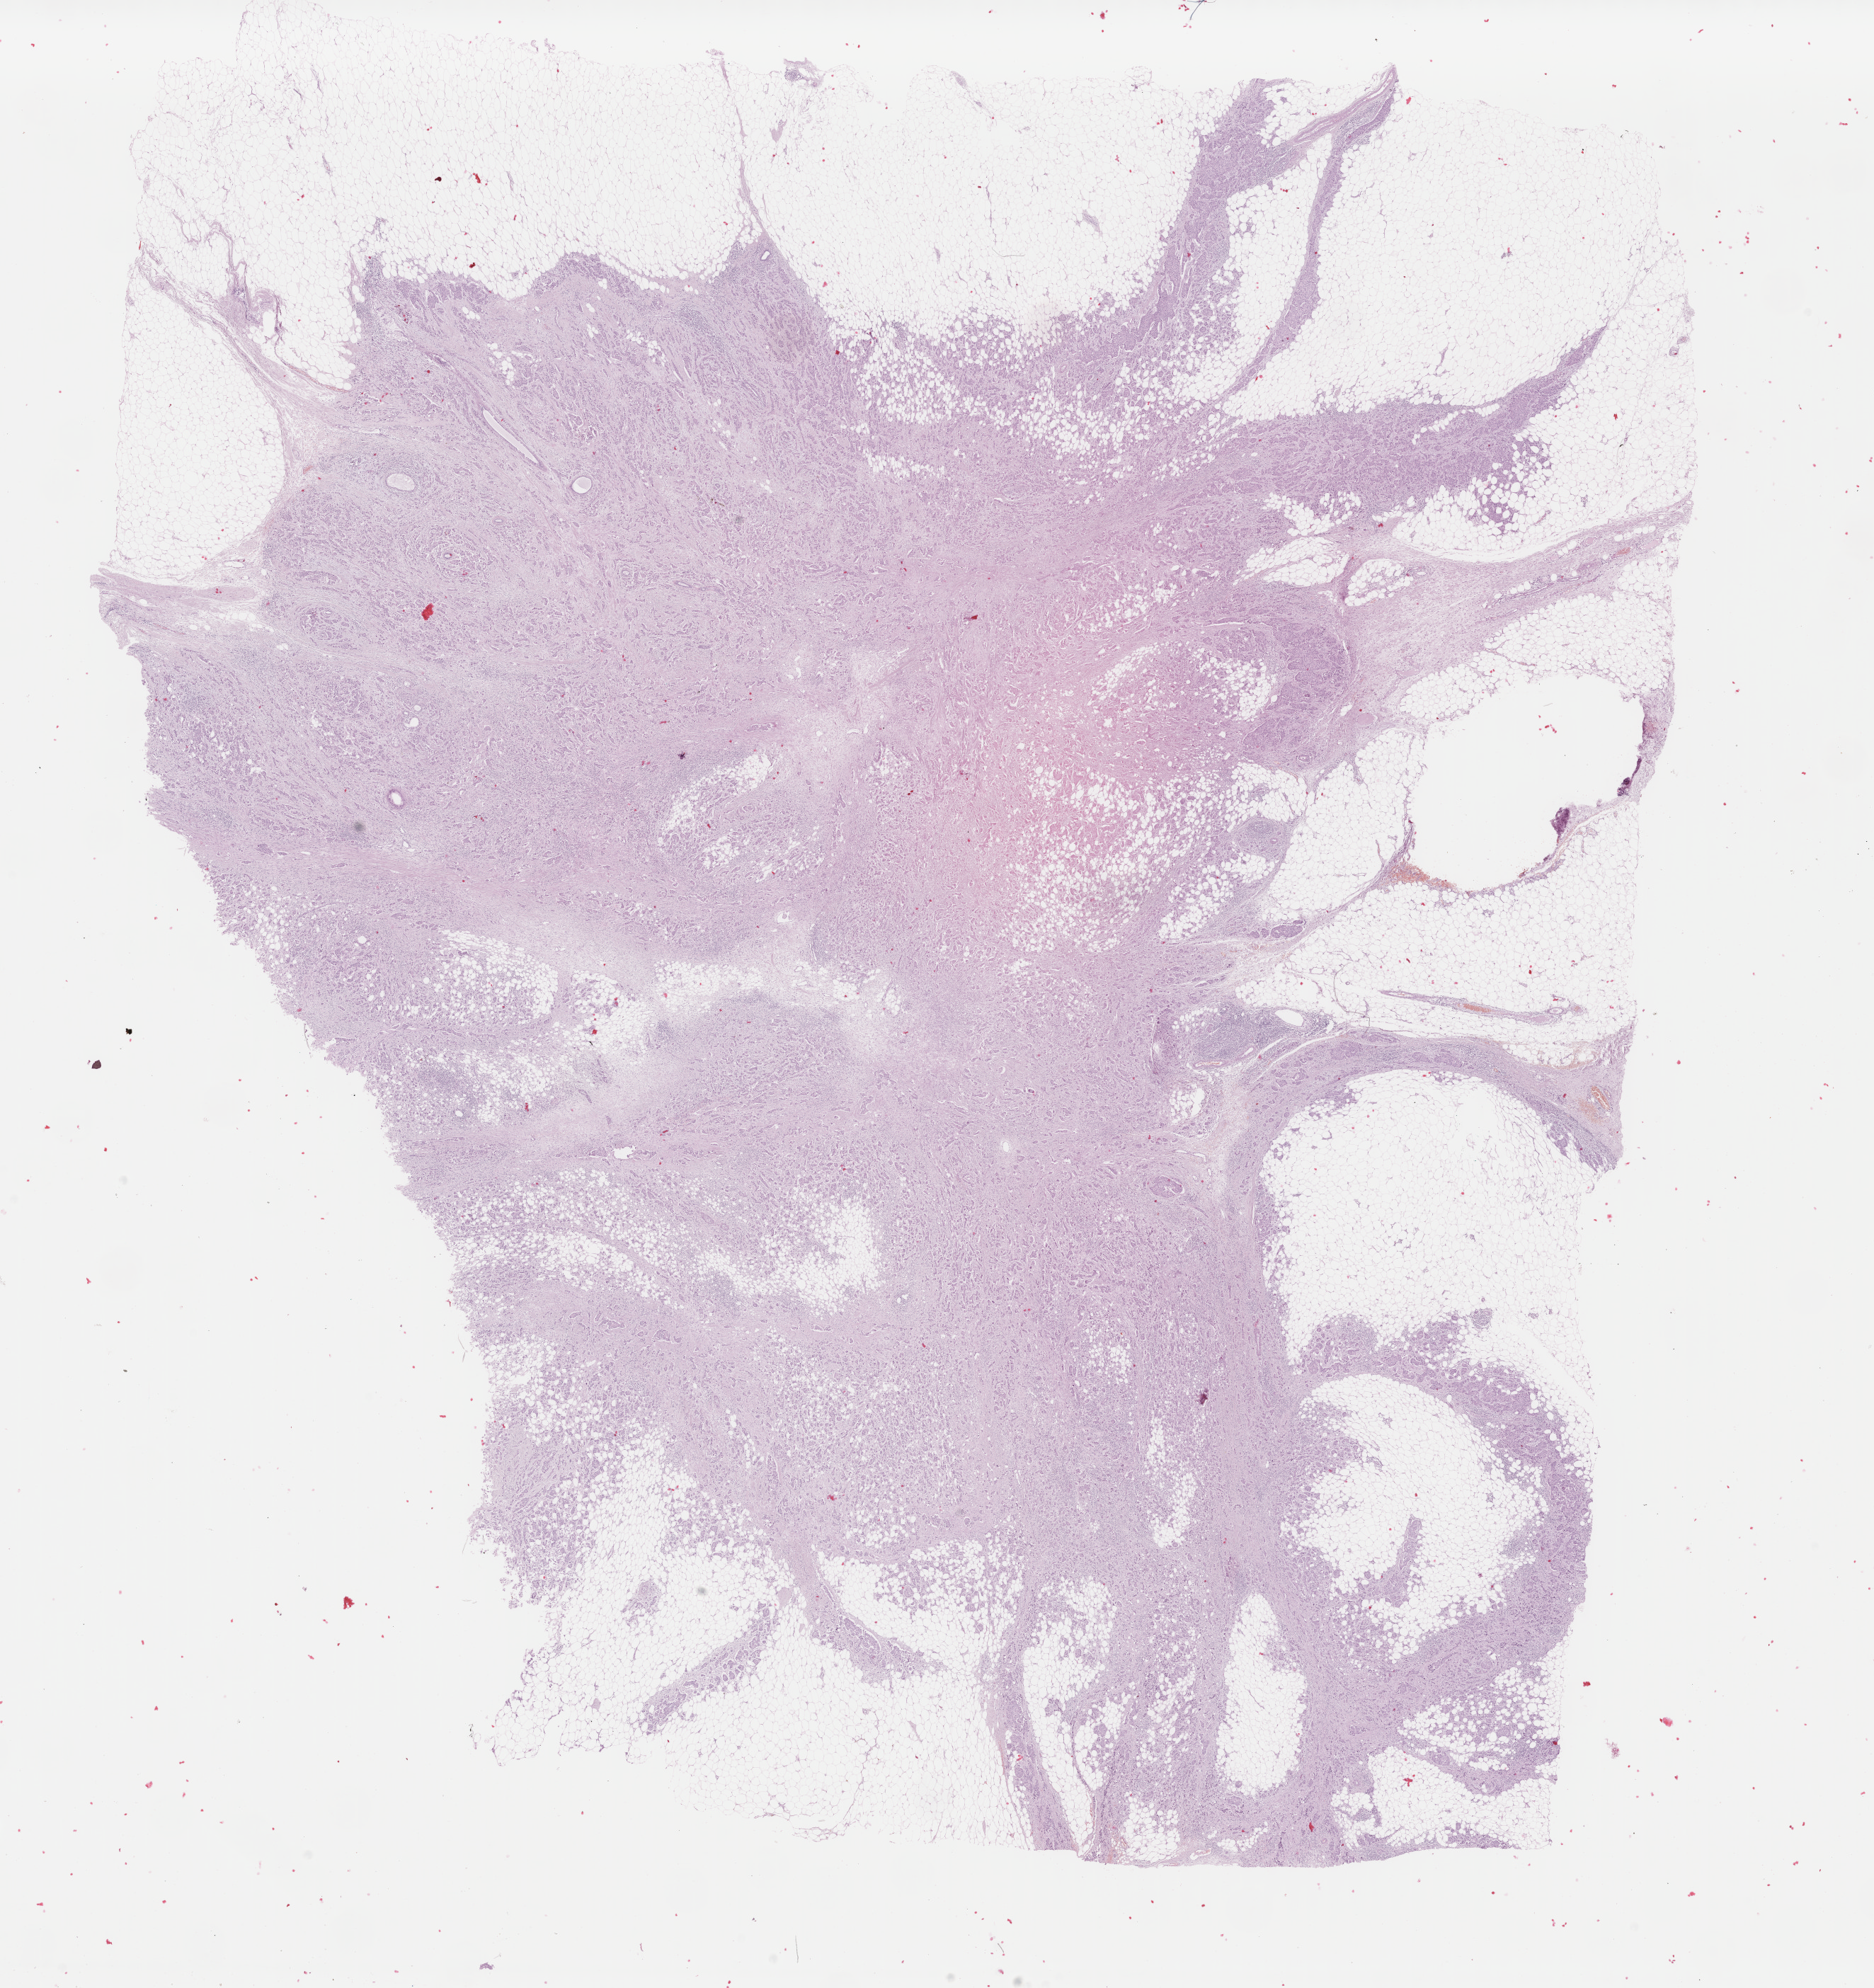
H&E whole-slide image — a low-resolution overview of the entire scanned area, about 21.0 x 22.3 mm (from a 40x scan), formalin-fixed paraffin-embedded (FFPE) diagnostic section, primary tumour sample from the breast. Female, age 54 years at initial diagnosis.
- histologic diagnosis: Infiltrating duct carcinoma, NOS
- lymph nodes positive (case pathology): 0 of 1 examined
- AJCC pathologic stage: IIA (7th edition)
- TNM: T2 N0 M0